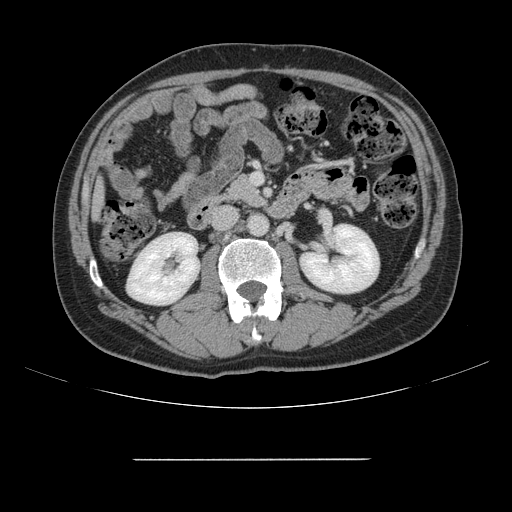
Contrast-enhanced abdominal CT, one axial slice. Position 51 of 164 along the scan axis. Intravenous contrast given. Soft-tissue window (W 400 / L 40 HU). 2.5 mm slice thickness. 512 × 512 image matrix. Male patient, age 54 years. From the clinical record (not read from this slice): diagnosis: colorectal cancer liver metastases, imaged before liver resection.
Annotated regions visible in this slice (expert manual segmentation):
- liver: bounding box <95,186,102,211> (left, top, right, bottom; pixels)
- planned liver remnant (the part of the liver to remain after resection): <96,188,102,213>